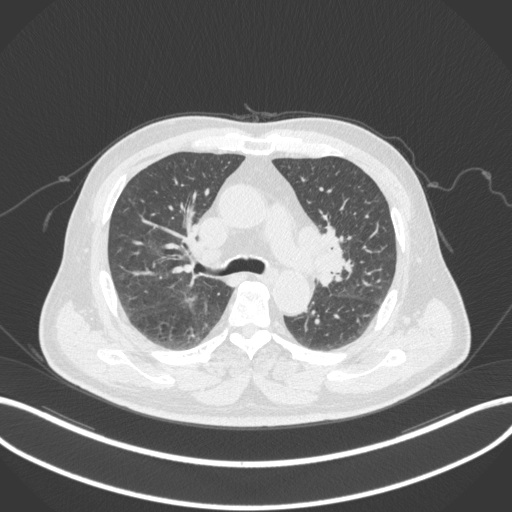
Chest CT, one axial slice; slice 189 of 286 in the series (ordered by position); lung window (W 1500 / L -600 HU); 1 mm slice thickness; 512 × 512 image matrix, field of view 400 × 400 mm. Patient: male, 67 years. From the clinical record (not read from this slice): clinical TNM (as recorded): T2a N1 M0; histopathological grade: G3.
Structures marked on this image (rectangle marked by the reading radiologist):
- lung tumour (recorded histology: adenocarcinoma): box from (x=310, y=235) to (x=350, y=288) px